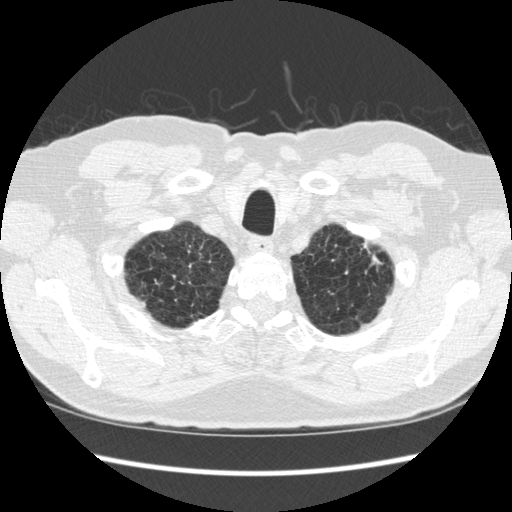
Axial slice from a low-dose chest CT screening exam; second screening round (one year after baseline); lung window (W 1500 / L -600 HU); standard (soft-tissue) reconstruction kernel (STANDARD); slice 32 of 295 in the series. Male participant, aged 70 years at enrolment.
Expert-annotated lung lesion, box from (x=324, y=233) to (x=388, y=303) px. The screening reader recorded 5 non-calcified nodules or masses ≥4 mm on this exam; which of them this box marks is not recorded. Official screen result: positive, change unspecified: nodule(s) >= 4 mm or enlarging nodule(s), mass(es), or other non-specific abnormalities suspicious for lung cancer. Participant outcome: lung cancer diagnosed 479 days after this screen — squamous cell carcinoma, NOS, left upper lobe, moderately differentiated (G2), stage IA (AJCC 6th edition), 18 mm at pathology.